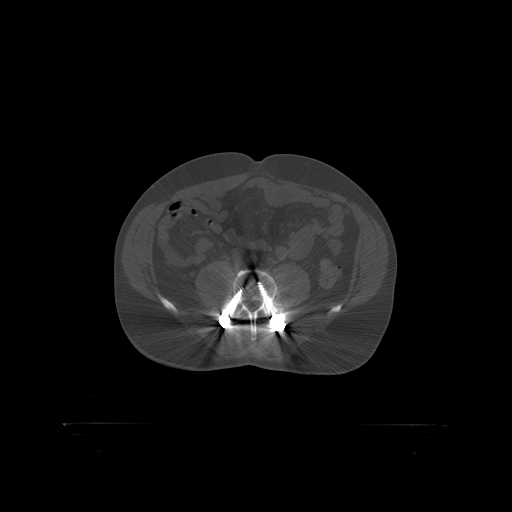
CT including the spine, one axial slice; position 213 of 399 along the scan axis; reconstruction kernel STANDARD; 120 kVp; bone window (W 1800 / L 400 HU); 1.25 mm slice thickness; 512 × 512 image matrix, field of view 650 × 650 mm. Male patient, age 46 years. From the clinical record (not read from this slice): primary cancer: skin.
Outlined on this slice (semi-automatic segmentation, software-assisted and operator-edited):
- L4 vertebra: bounding box [x1, y1, x2, y2] px = [236, 314, 270, 318]
- L5 vertebra: [221, 271, 290, 319]